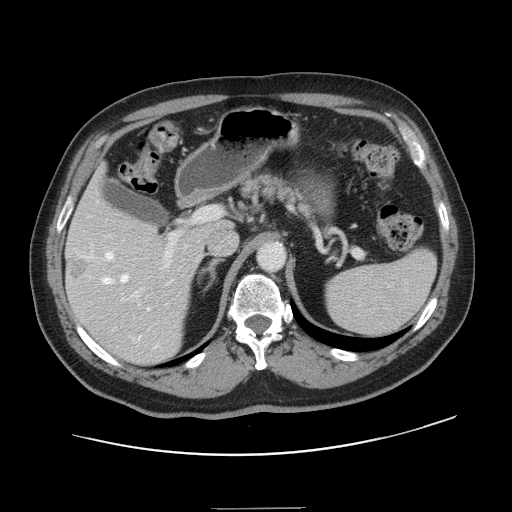
Contrast-enhanced abdominal CT, one axial slice. Slice 88 of 143 in the series (ordered by position). Intravenous contrast given. Soft-tissue window (W 400 / L 40 HU). 2.5 mm slice thickness. 512 × 512 image matrix, field of view 402 × 402 mm. Male patient, age 62 years. Case-level facts recorded for this patient, not image findings: diagnosis: colorectal cancer liver metastases, imaged before liver resection; multiple liver metastases: yes; largest metastasis: 2.7 cm; disease in both lobes: no.
Structures marked on this image (outlined manually by an expert reader):
- hepatic veins: bounding box (x1, y1, x2, y2) in pixels: (83, 253, 157, 347)
- liver: (67, 170, 225, 363)
- planned liver remnant (the part of the liver to remain after resection): (68, 173, 228, 244)
- portal vein (with intrahepatic branches): (79, 207, 220, 340)
- liver metastasis: (68, 258, 91, 280)